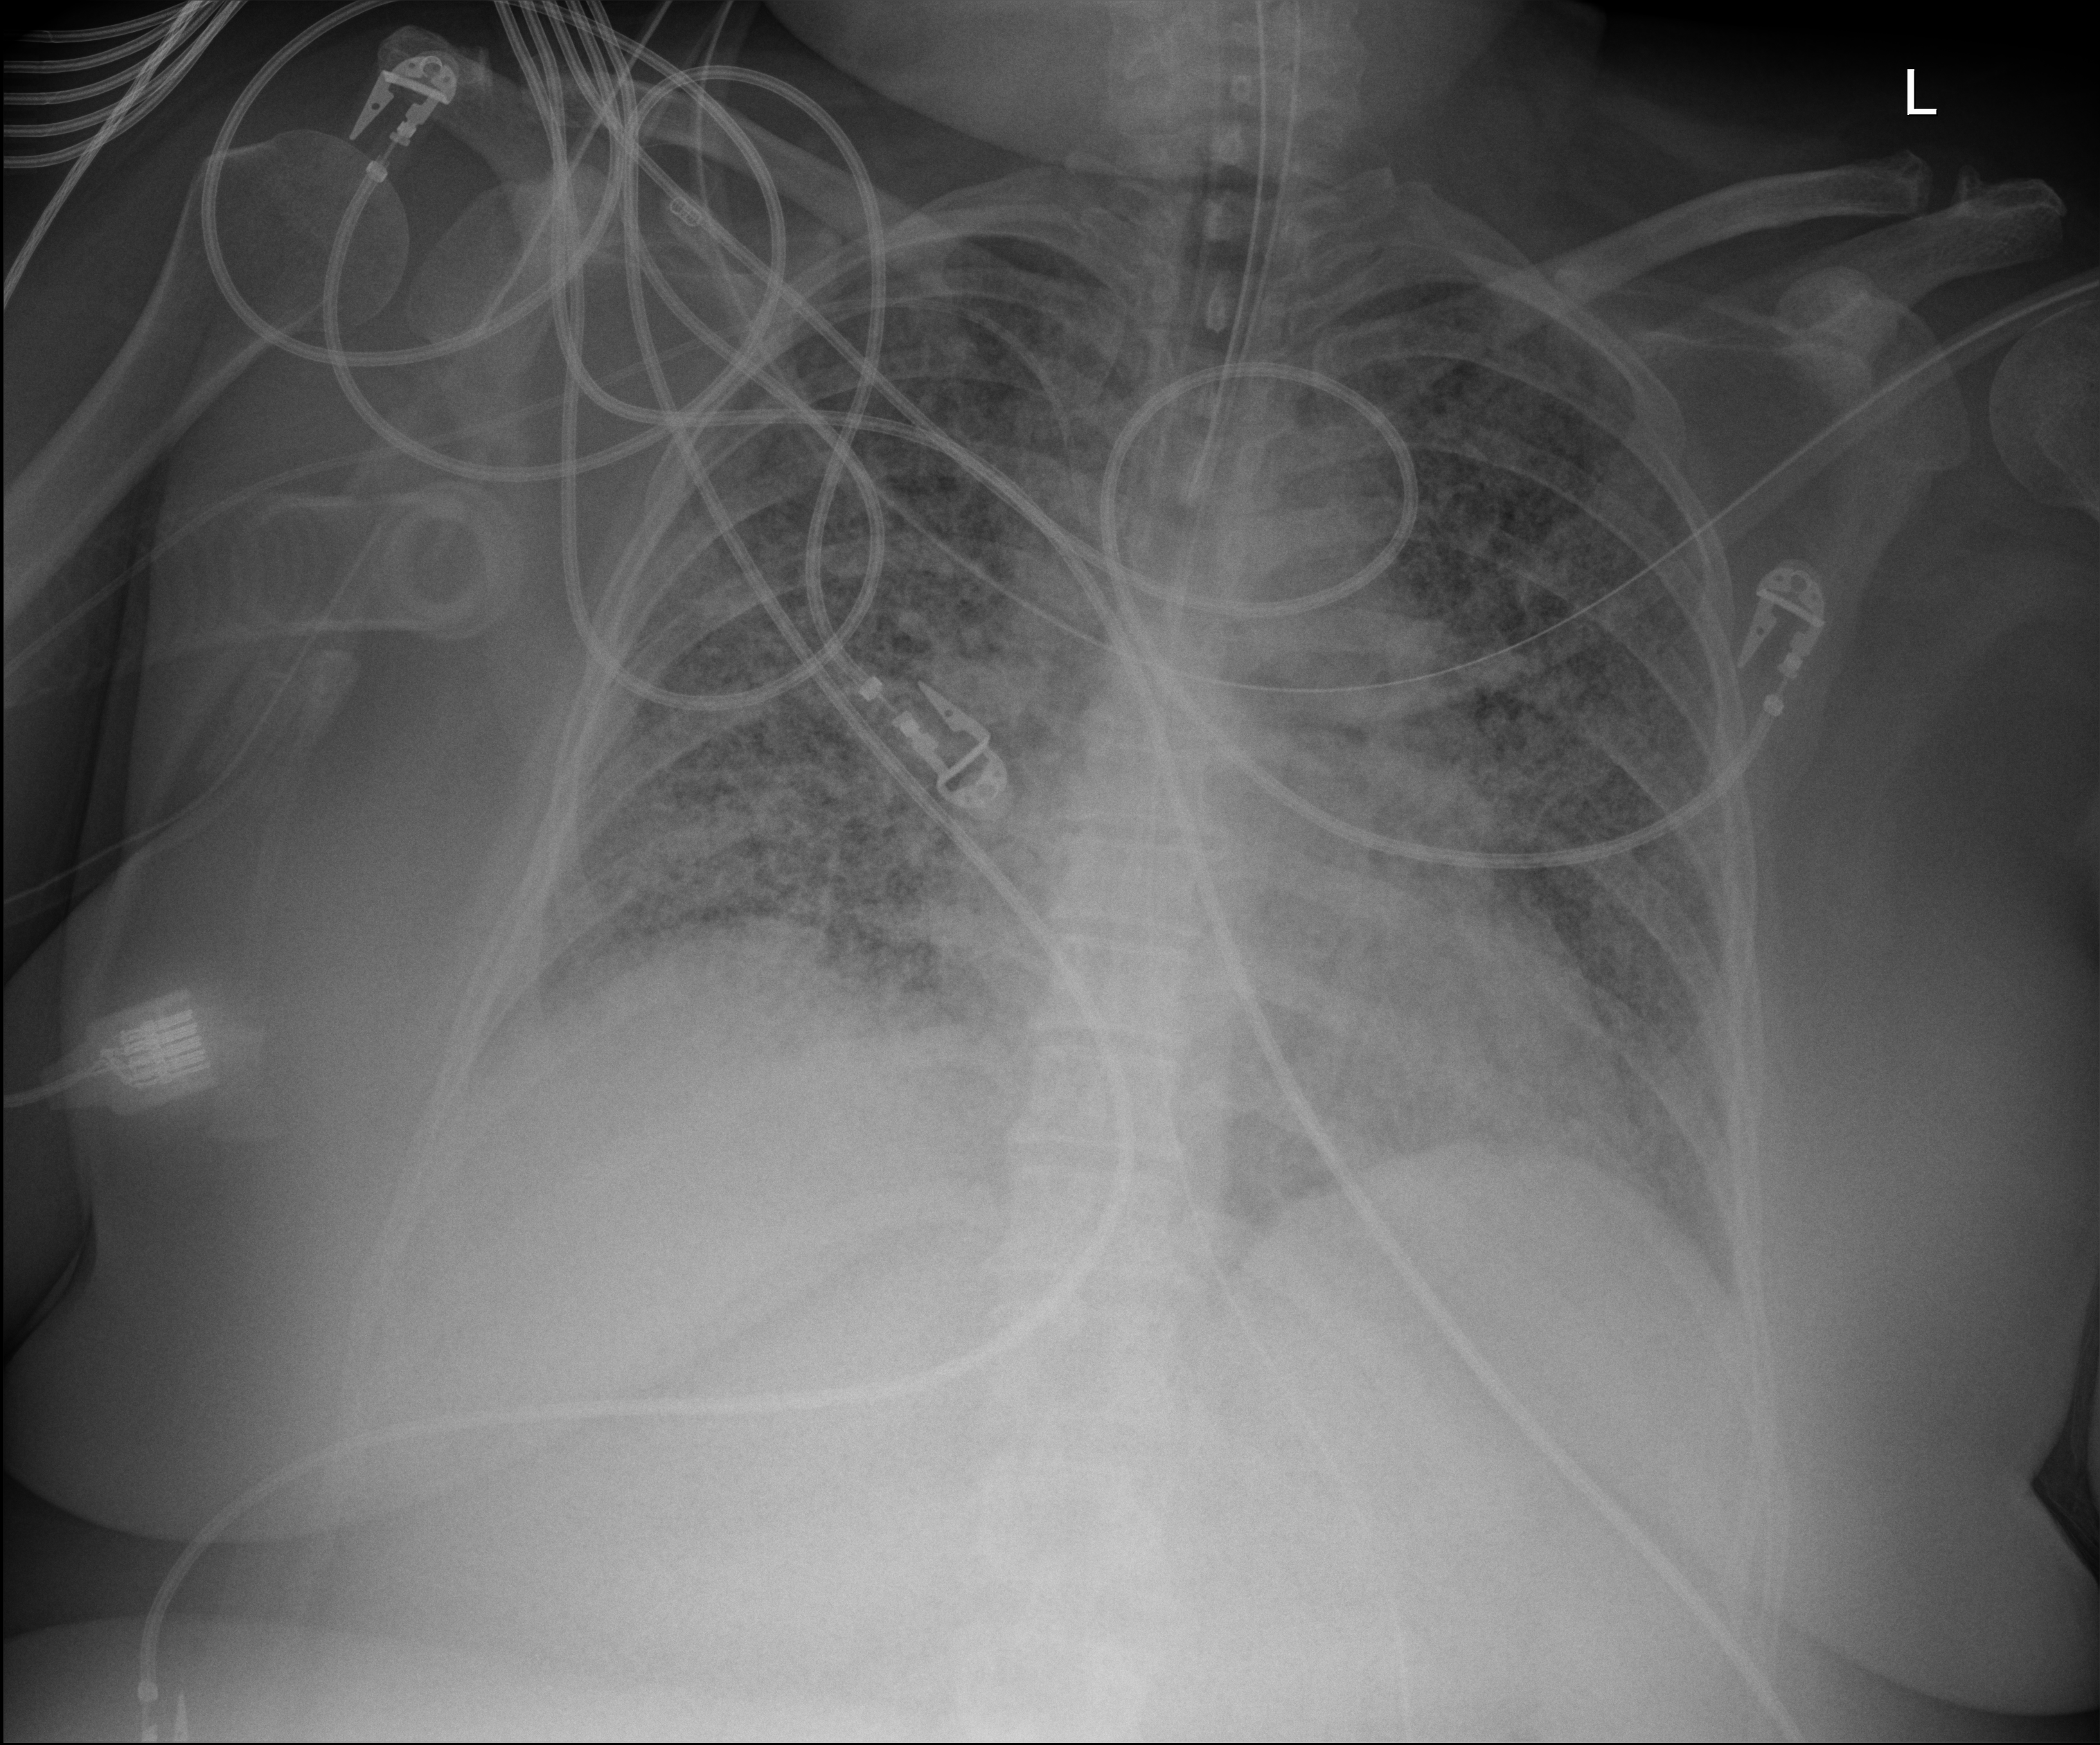
Chest X-ray (portable); anteroposterior (AP) projection. Patient hospitalised with COVID-19; female, aged 18–59 years.
Hospital-stay facts (about this admission, not read from this image; timing relative to this image not recorded):
- mechanically ventilated during this hospital stay: yes
- hypertension (admission record): yes
- admitted to intensive care during this hospital stay: yes